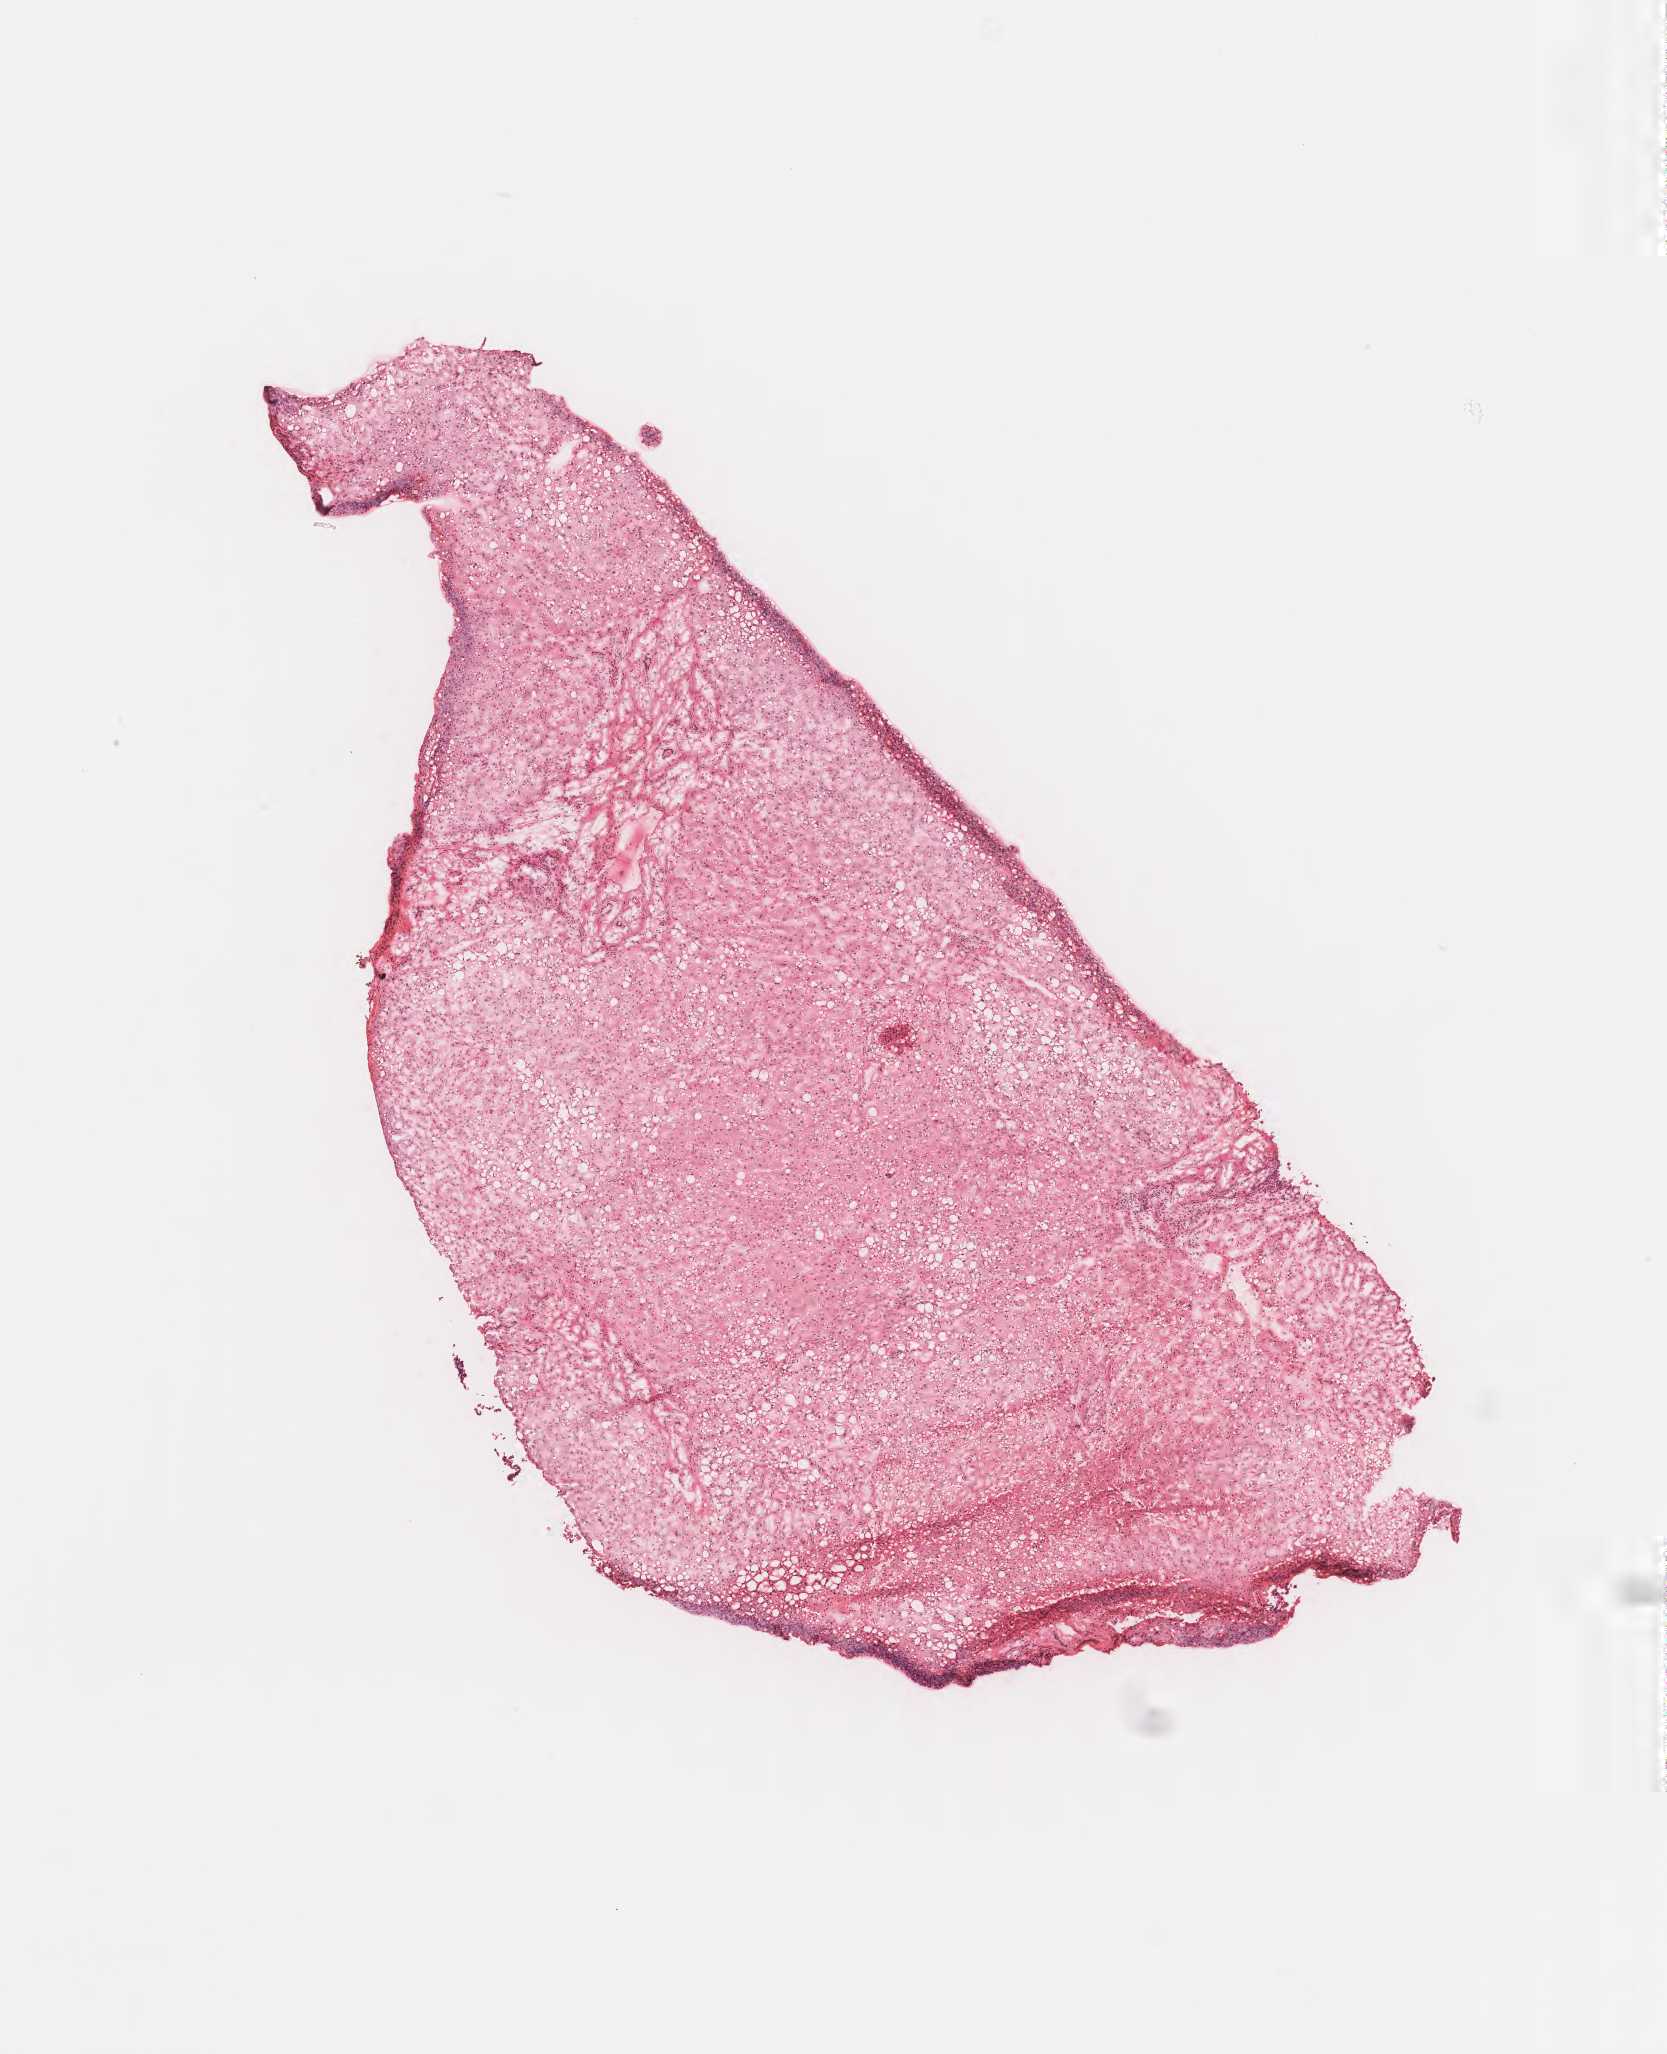
H&E whole-slide image — low-resolution overview of the scanned area, about 6.6 x 8.1 mm. Frozen section (tissue freezing medium). Specimen: non-tumor (normal tissue) sample from a patient with hepatocellular carcinoma, NOS. Site: liver. Male patient; age at initial diagnosis 86 years. Pathologist review of this section (percent, as recorded): tumor cells 0%, tumor nuclei 0%, stromal cells 10%, necrosis 0%, normal cells 90%. Infiltration values recorded for this section: lymphocyte infiltration 4%, monocyte infiltration 1%, neutrophil infiltration 2%.
This section: non-tumor tissue sample; the patient's diagnosis is given above. Section: top of the tissue portion.